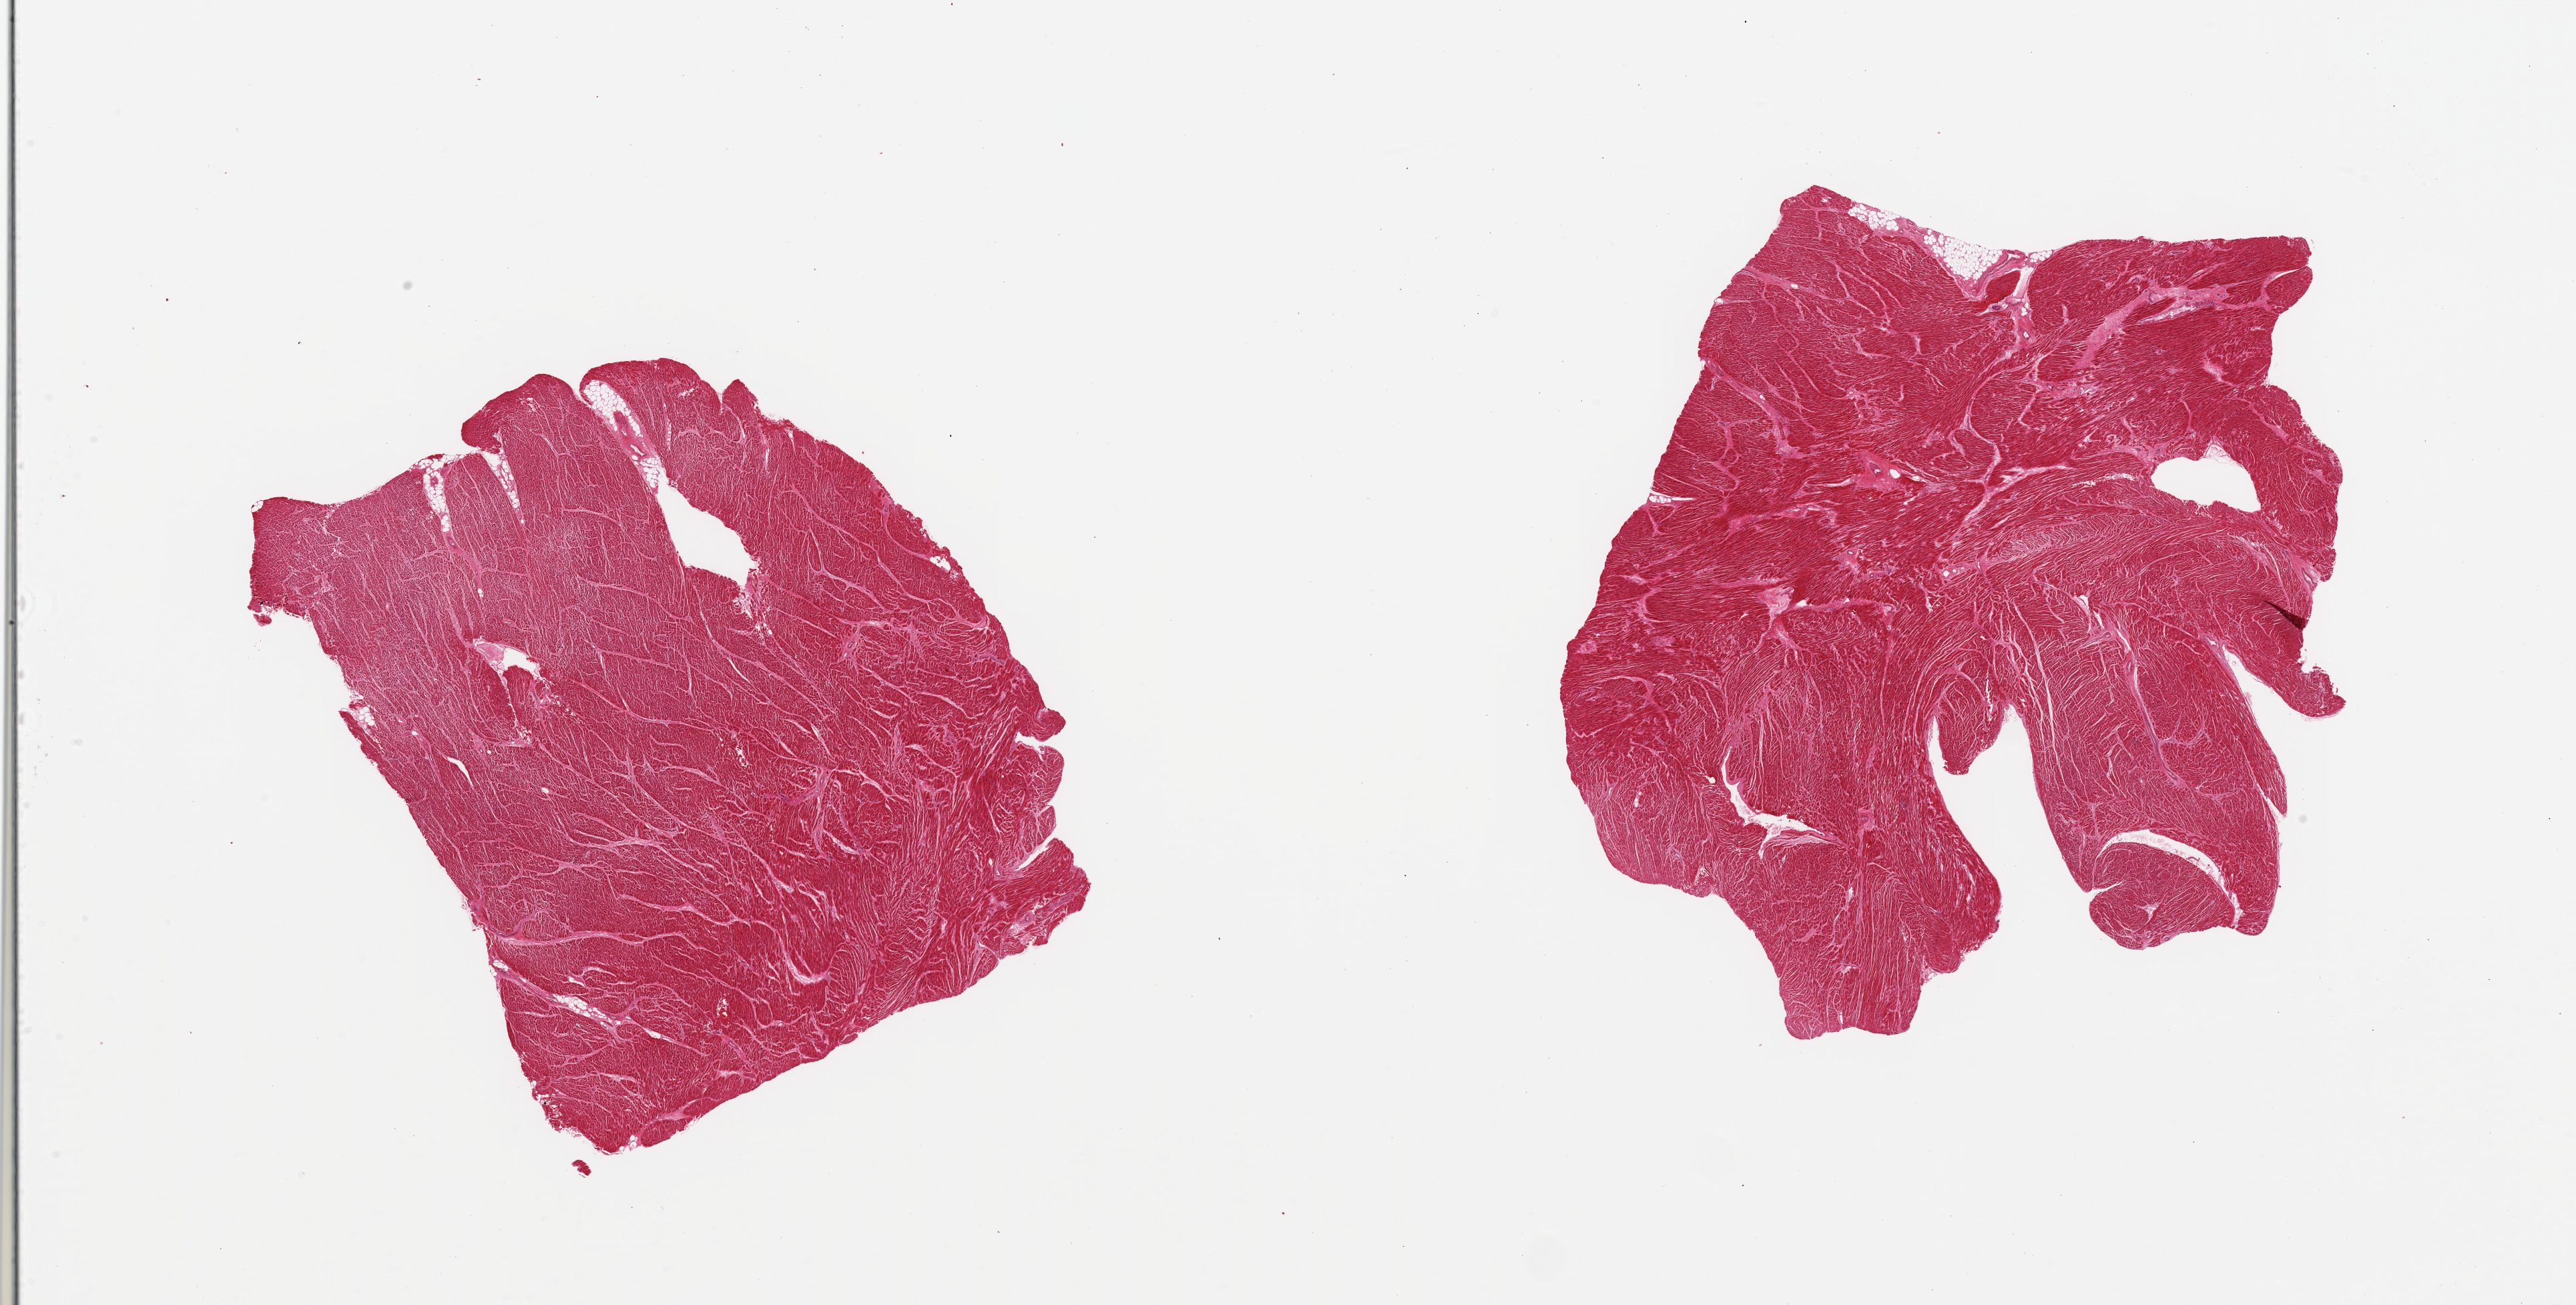
Whole-slide image, H&E stain, whole scanned area (about 30.5 x 15.5 mm) shown as a low-resolution overview. PAXgene-fixed paraffin-embedded (PFPE) section. Sampled site (target tissue): heart. Donor tissue sample. Donor: female.
Pathologist's review note for this sample: 2 pieces, moderate/marked interstitial fibrosis/ischemic changes.